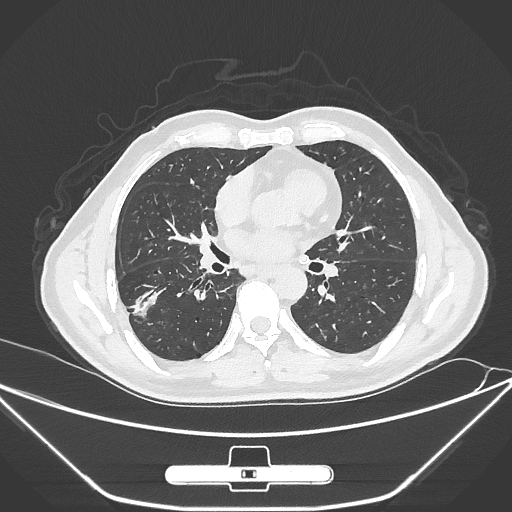
Chest CT, one axial slice. Slice 145 of 310 in the series (ordered by position). Reconstruction kernel IMR1,SharpPlus. Lung window (W 1500 / L -600 HU). 1 mm slice thickness. 512 × 512 image matrix, field of view 398 × 398 mm. Male patient, age 71 years. Case-level facts recorded for this patient, not image findings: clinical TNM (as recorded): T1c N0 M0; histopathological grade: G2.
Structures marked on this image (rectangle marked by the reading radiologist):
- lung tumour (recorded histology: adenocarcinoma): box from (x=131, y=285) to (x=166, y=332) px